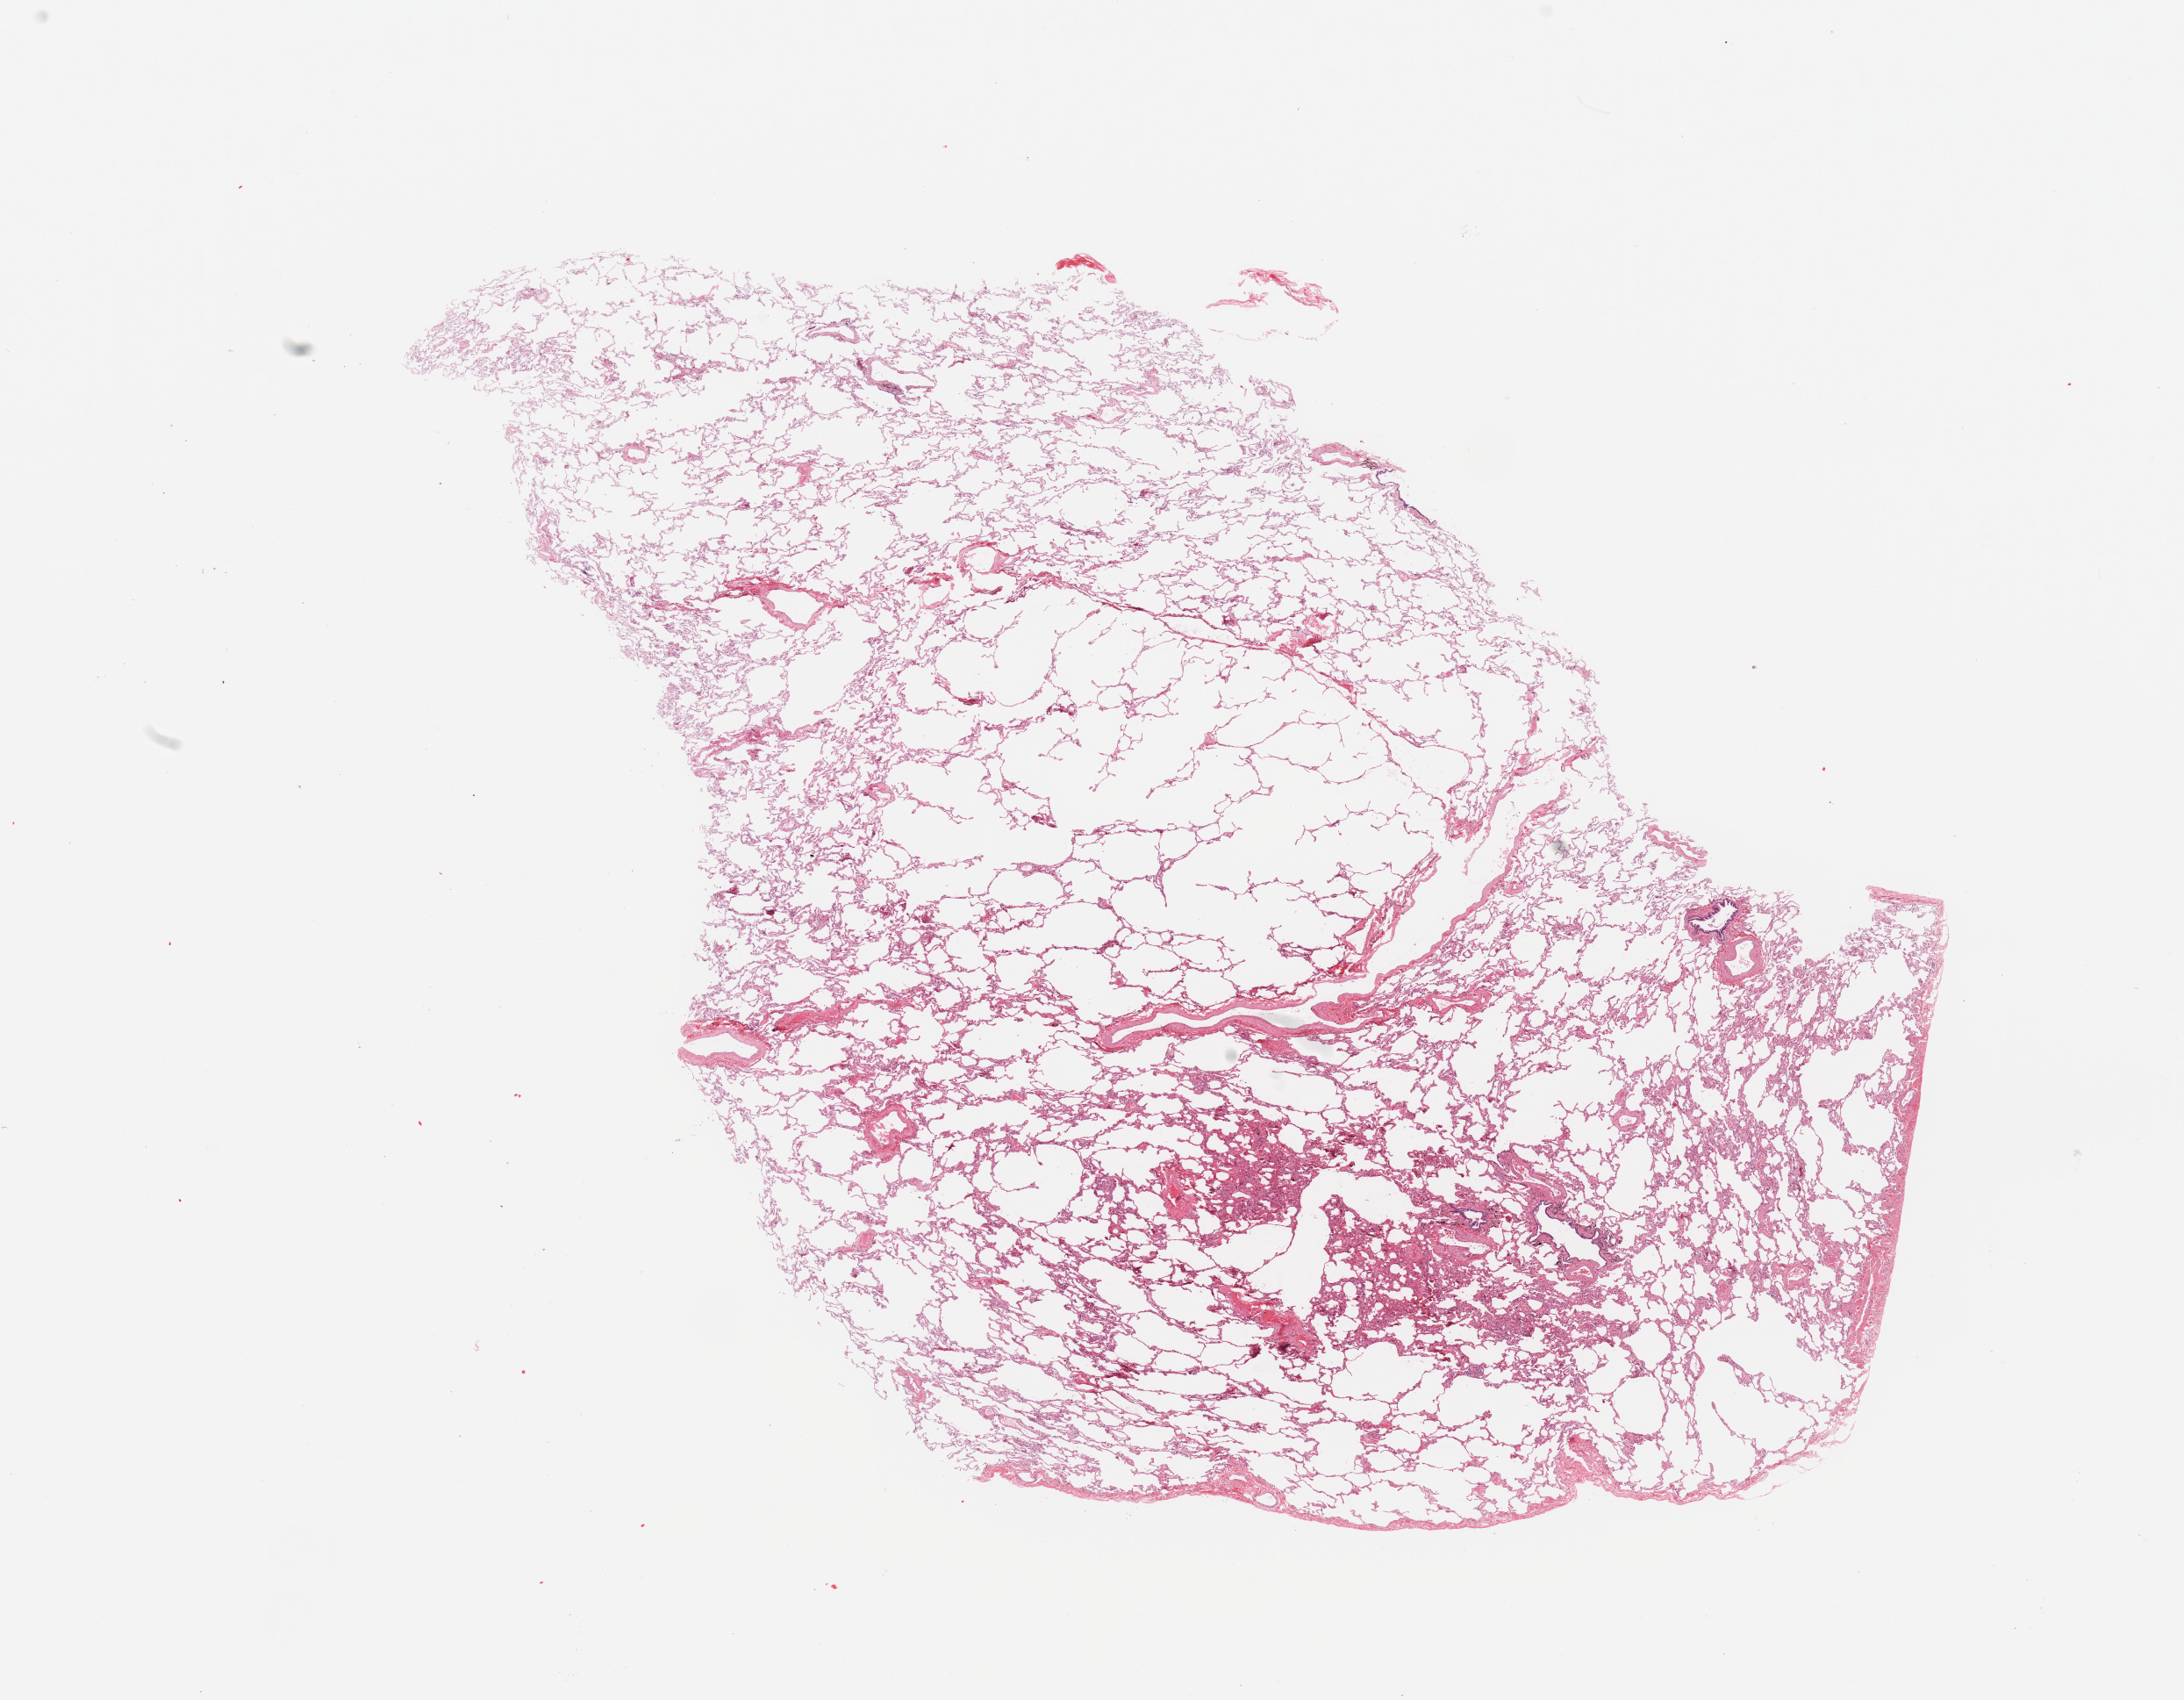
H&E-stained whole-slide image — a low-resolution overview of the entire scanned area, about 19.7 x 15.3 mm (slide scanned at 20x); normal (non-tumour) tissue sample, sampled site: lung. Patient: male, age 67 years.
This section: normal (non-tumour) tissue from the same patient. Patient diagnosis: Adenocarcinoma, NOS.